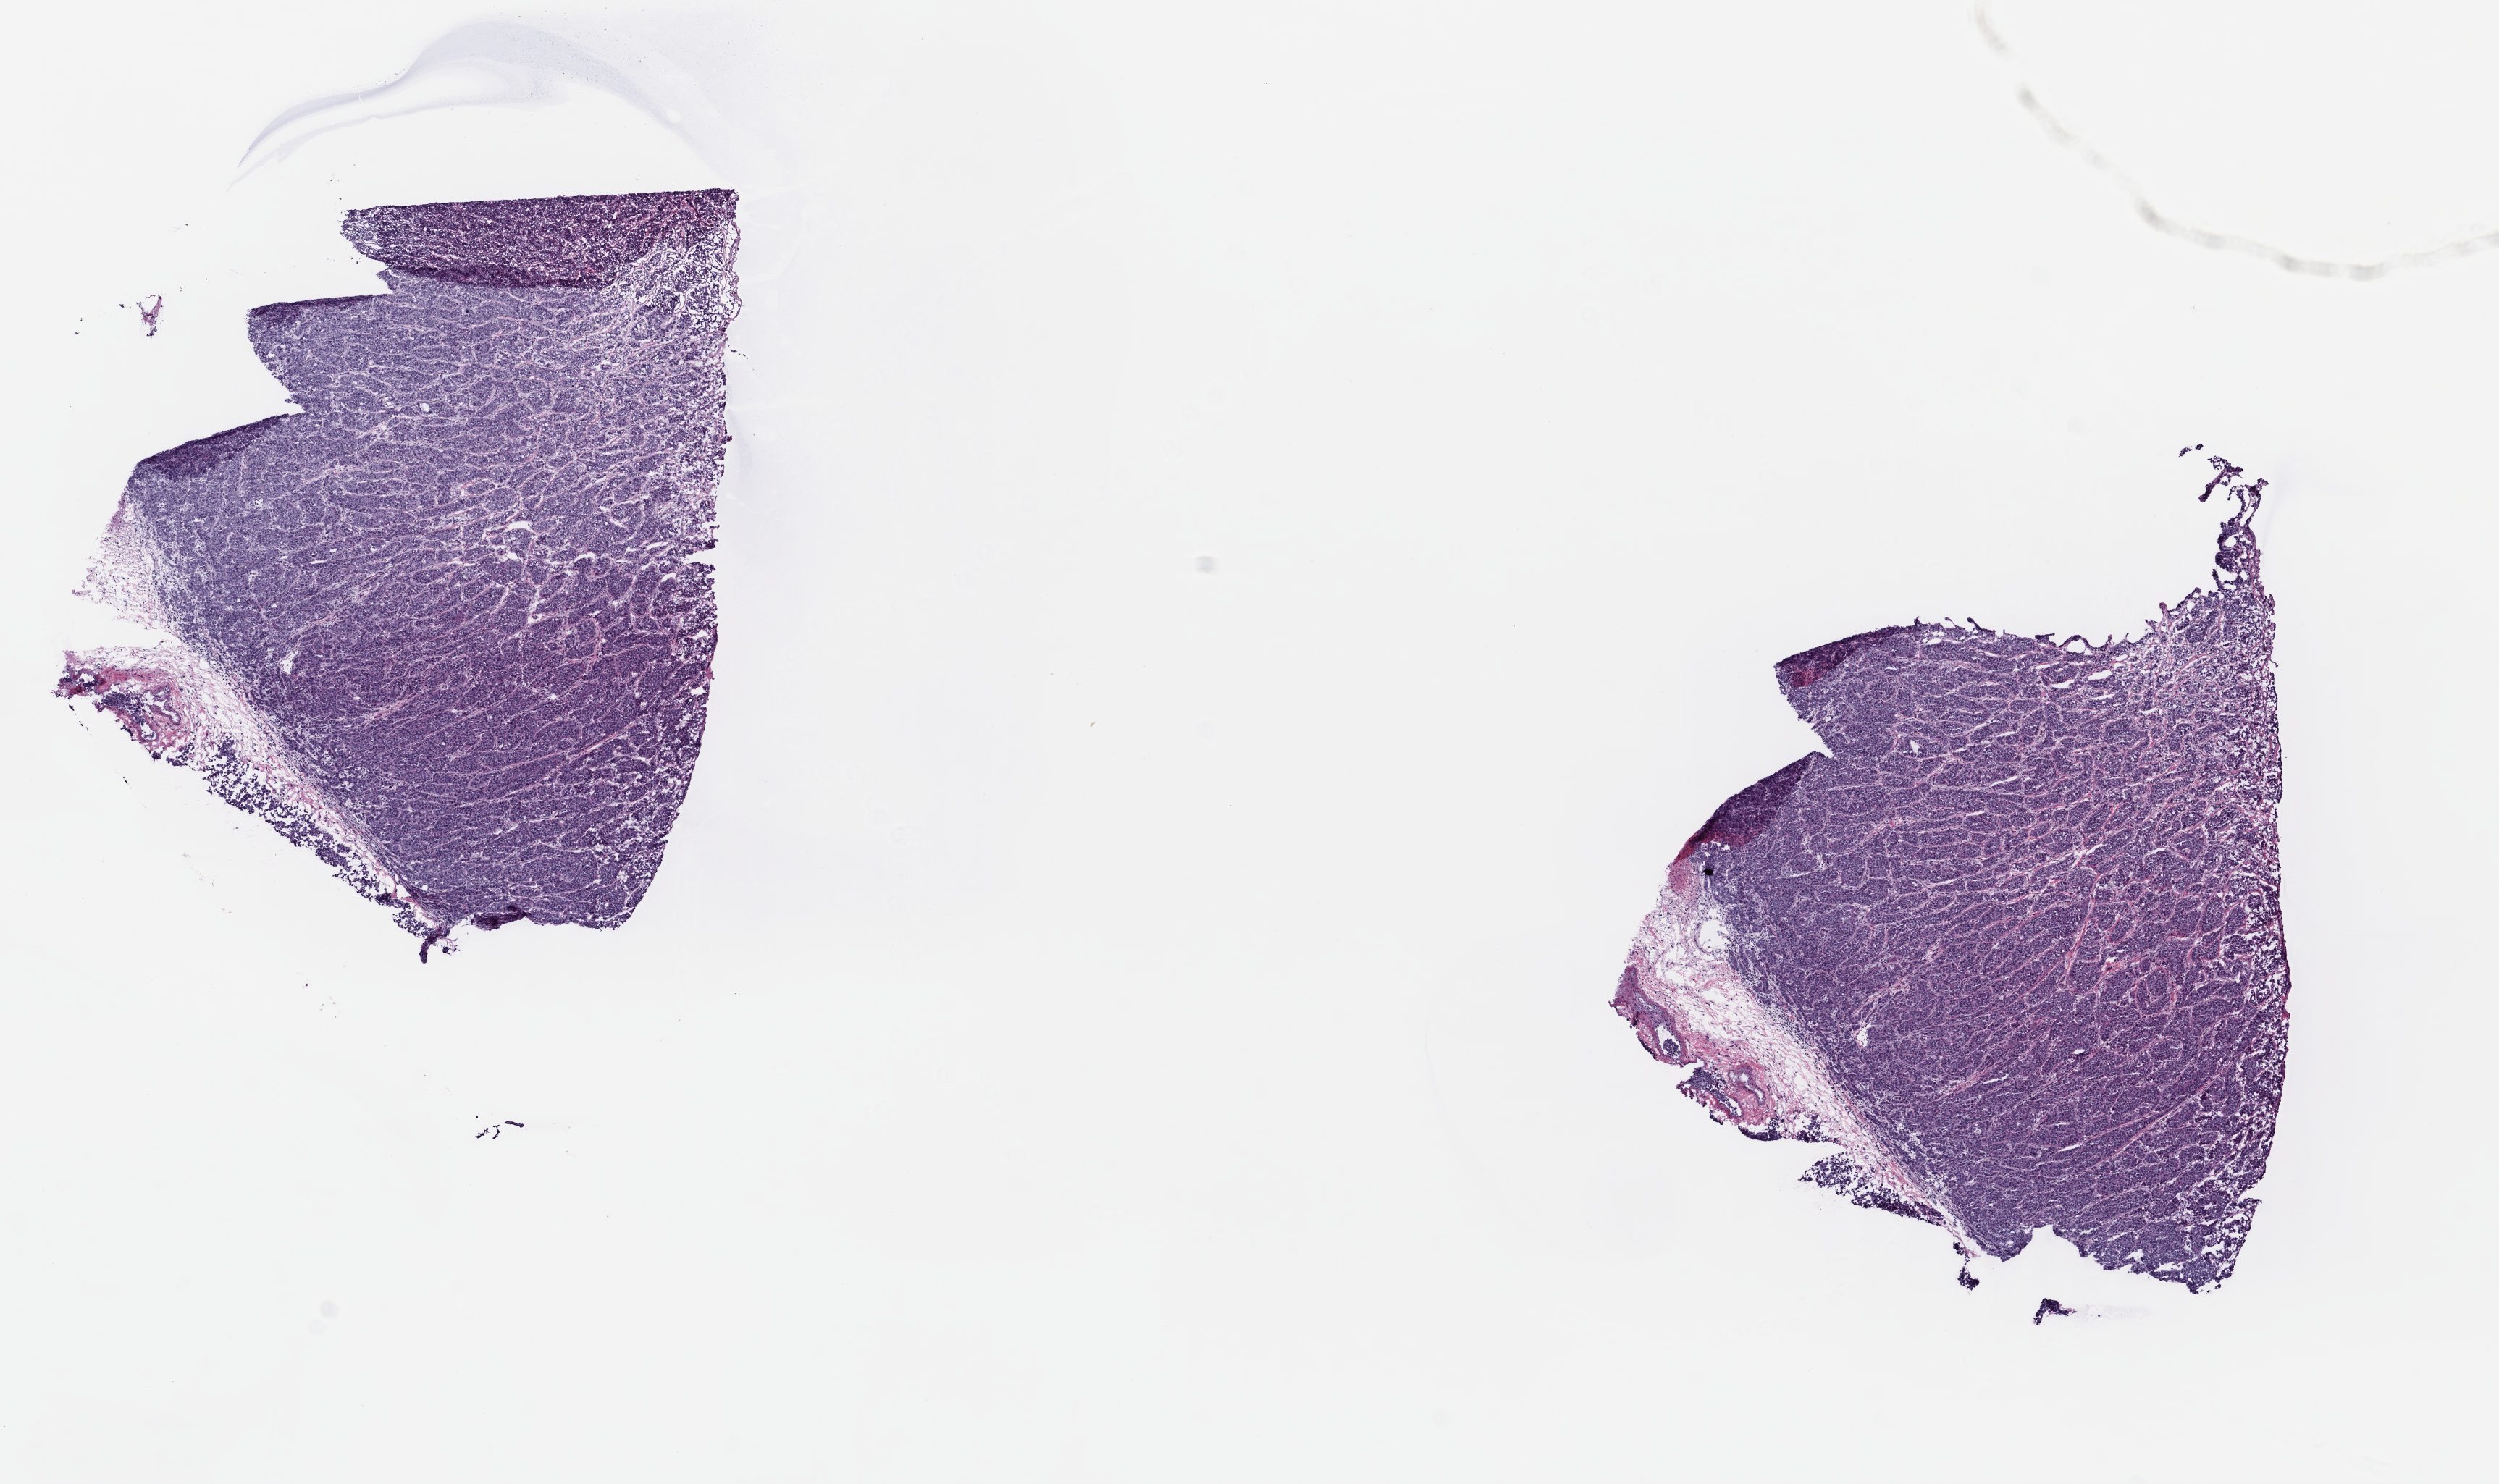
Whole-slide histology image, H&E-stained — a low-resolution overview of the entire scanned area, about 13.6 x 8.1 mm (slide scanned at 40x). Frozen section from the top of the tissue portion. Sample: primary tumour, breast. Female patient; age at initial diagnosis 80 years. Pathologist review of this section (percent, as recorded): tumour cells 90%, tumour nuclei 95%, normal cells 0%, stromal cells 10%, necrosis 0%. Inflammatory infiltration, as recorded: lymphocyte infiltration 0%, monocyte infiltration 0%, neutrophil infiltration 0%.
- histologic diagnosis: Infiltrating duct carcinoma, NOS
- laterality: left
- AJCC pathologic stage: IIIA (7th edition)